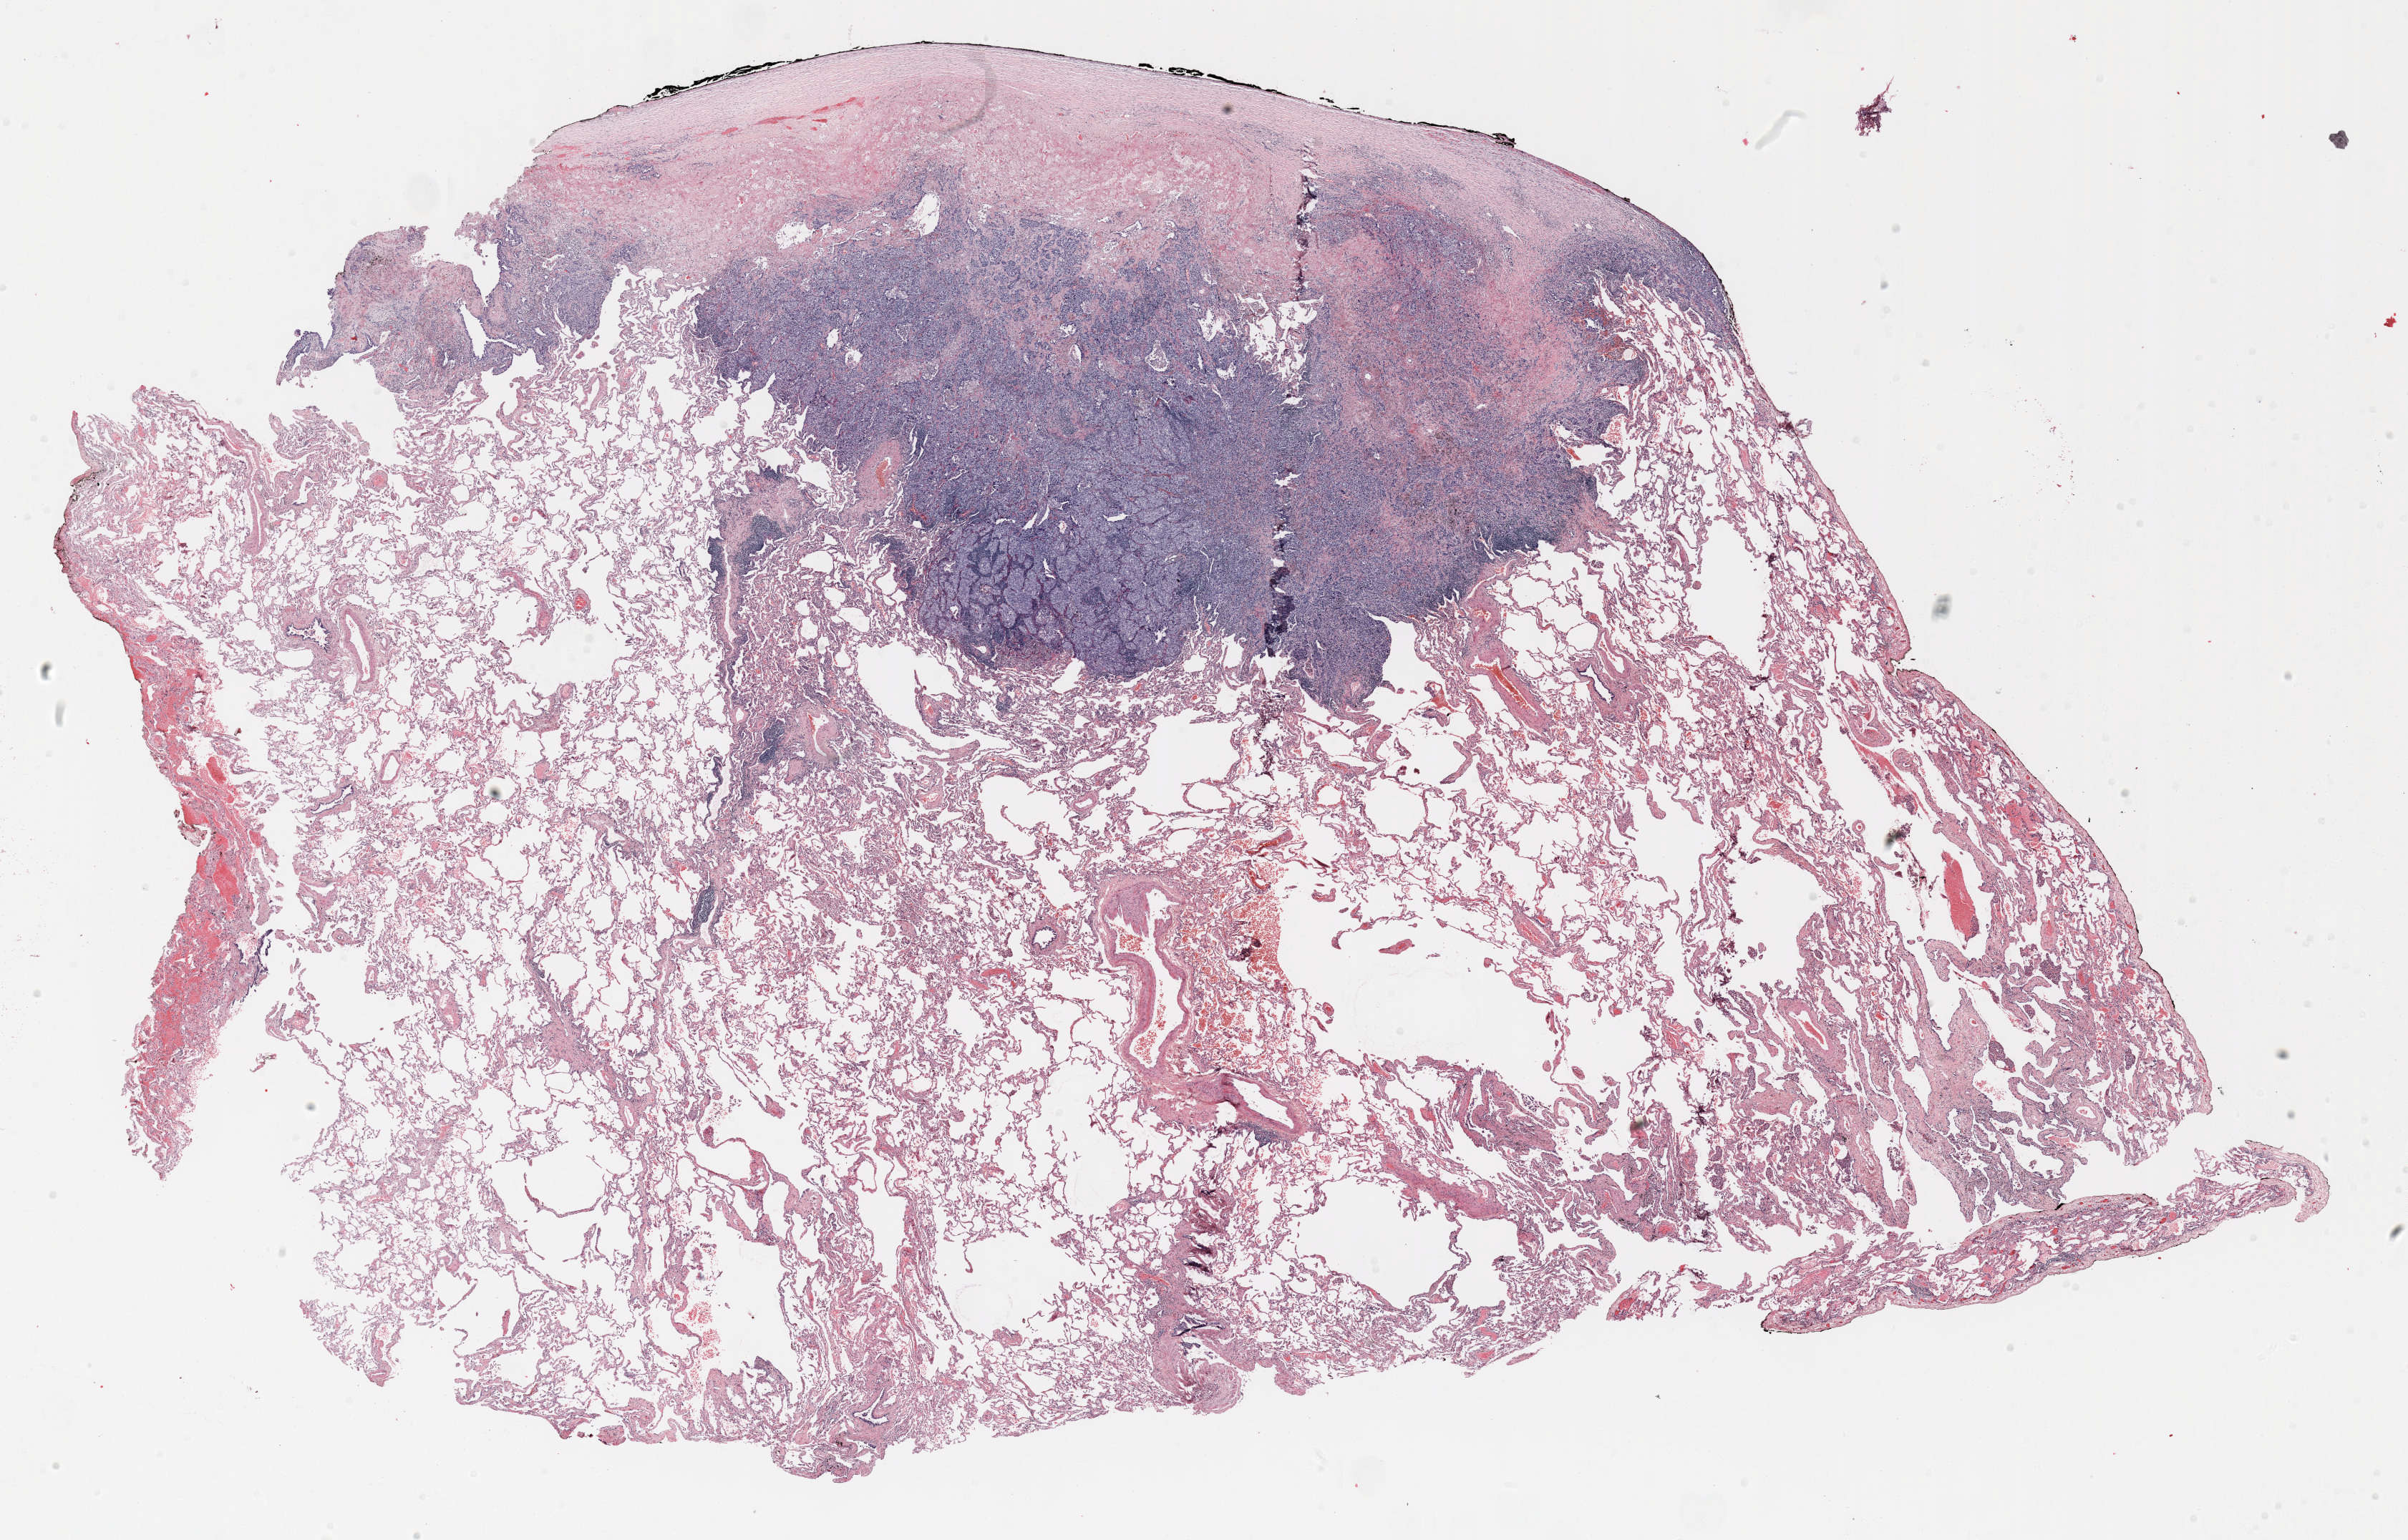
Whole-slide histology image, H&E-stained — a low-resolution overview of the entire scanned area, about 27.0 x 17.3 mm (from a 20x scan), FFPE section, lung. Female, age 56 at enrolment. Current smoker at enrolment. Grade: poorly differentiated (G3).
* tumour size (pathology): 15 mm
* primary tumour location (clinical record): right upper lobe
* ICD-O-3 topography: upper lobe of lung (C34.1)
* stage (AJCC 6th edition): IB
* participant's lung-cancer diagnosis: Large cell carcinoma, NOS